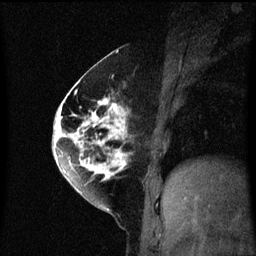
Breast MRI (dynamic contrast-enhanced), one sagittal slice; slice 27 of 60 in the series (ordered by position); dynamic contrast-enhanced series, image 2 of 3 at this slice position (ordered by acquisition); 1.5 T; TE 4.2 ms, TR 8.4 ms; 2 mm slice thickness; 256 × 256 image matrix, field of view 200 × 200 mm. Patient: female, 60 years.
Structures marked on this image (semi-automatic segmentation, software-assisted and operator-edited):
- analysis volume of interest (the breast-tissue region the enhancement analysis was run in; not a lesion): bounding box [x1, y1, x2, y2] px = [64, 70, 133, 195]
- tumour enhancement mask (voxels above the 70 % enhancement threshold inside the analysis volume of interest): [64, 80, 129, 193]